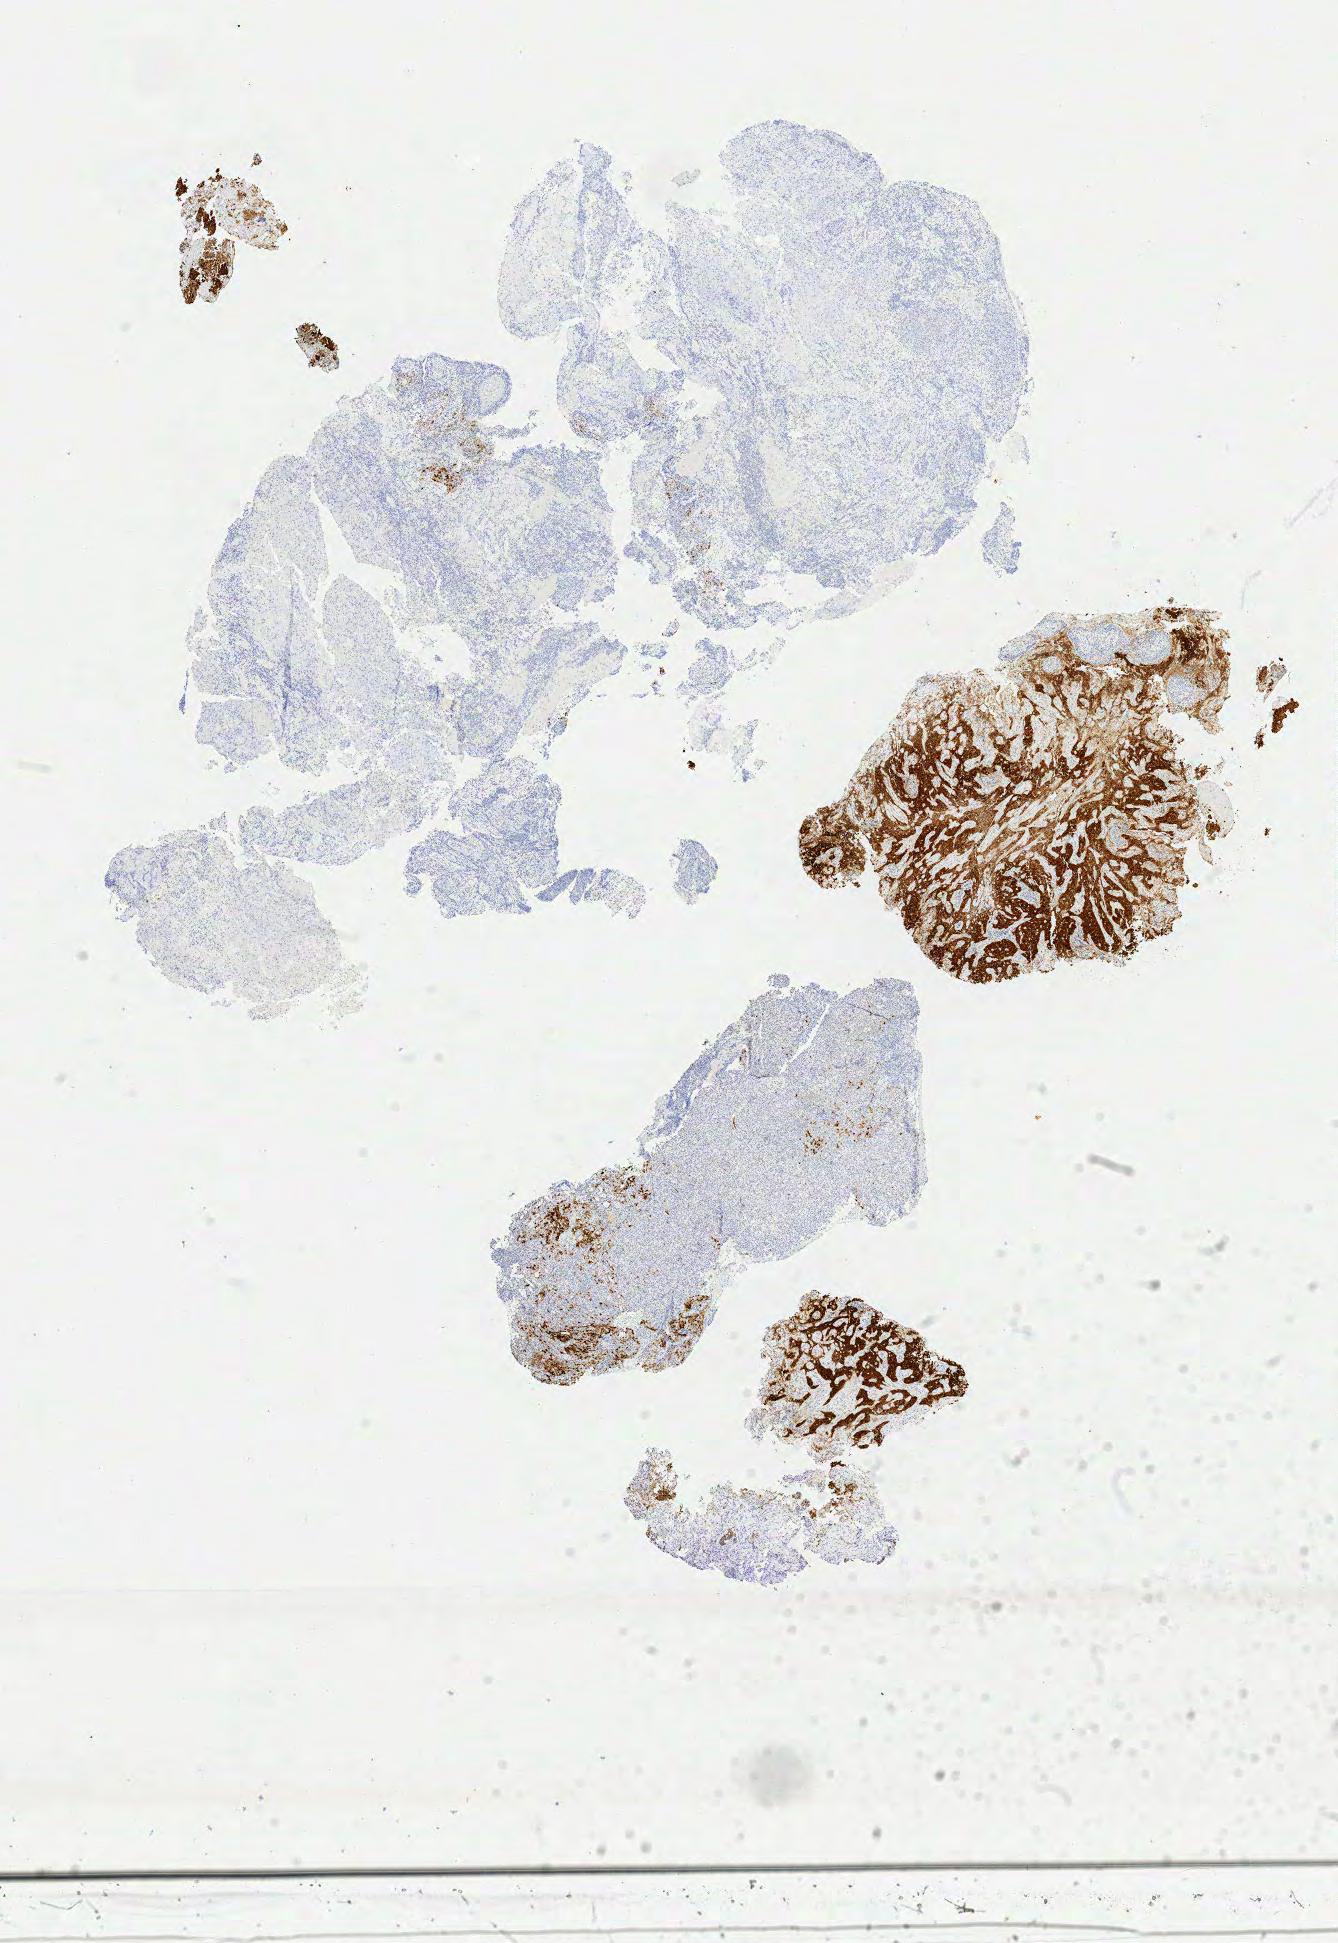
Whole-slide image, immunohistochemical stain for p16 (p16INK4a) — whole scanned area (about 10.7 x 15.5 mm) shown as a low-resolution overview; specimen: tumor tissue; anatomic site: cervix. Patient: female, age 63 years.
- diagnosis: Squamous cell carcinoma, large cell, nonkeratinizing, NOS